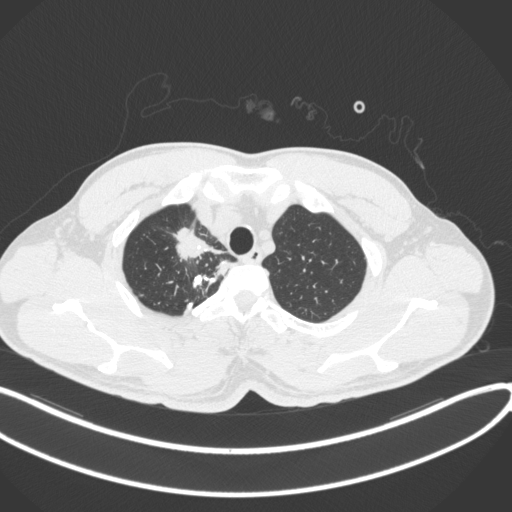
Chest CT, one axial slice. Slice 326 of 391 in the series (ordered by position). Reconstruction kernel B31f. 120 kVp. Lung window (W 1500 / L -600 HU). 512 × 512 image matrix, field of view 400 × 400 mm. Male patient, age 48 years. Case-level facts recorded for this patient, not image findings: clinical TNM (as recorded): T1c N1 M1.
Structures marked on this image (bounding box drawn by a radiologist):
- lung tumour (recorded histology: adenocarcinoma): bounding box [x1, y1, x2, y2] px = [169, 224, 230, 264]